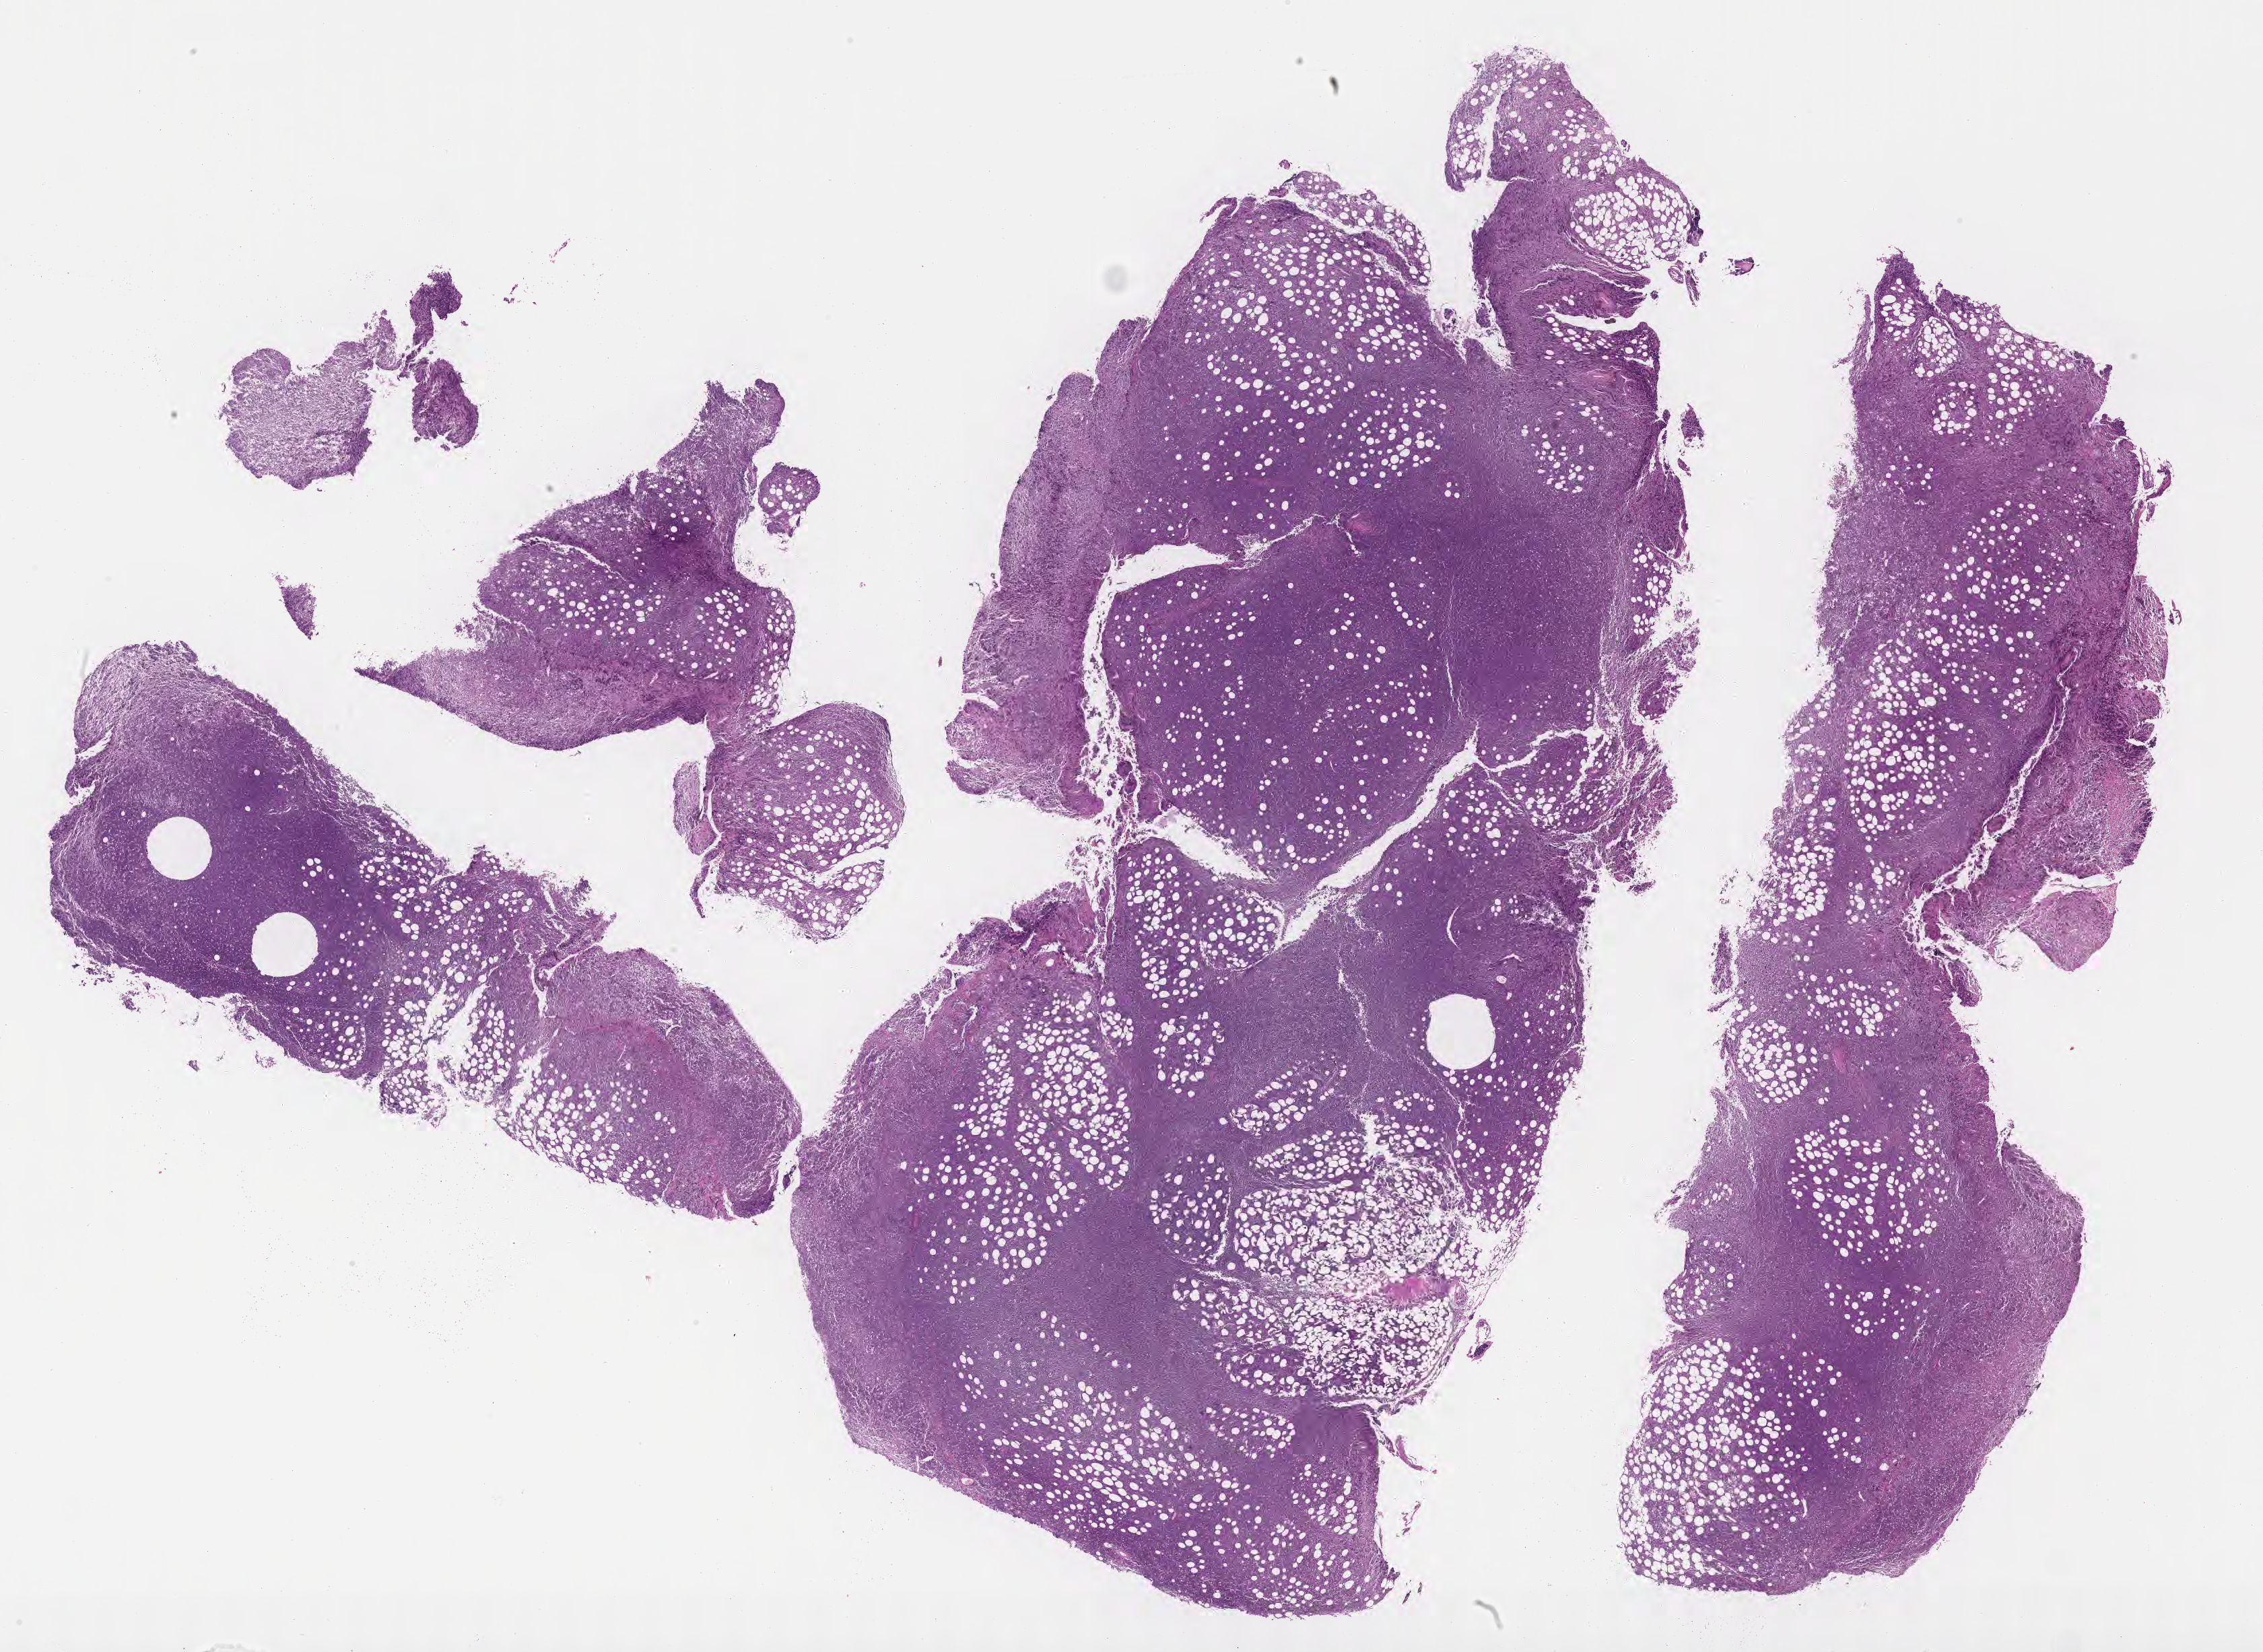
Digitized haematoxylin and eosin-stained section — low-resolution overview of the scanned area, about 27.2 x 19.8 mm, FFPE section, specimen: primary tumor. Male patient, 31 years old. Composition of this section per pathologist review: tumor cells 85%, tumor nuclei 95%, stromal cells 5%, necrosis 5%, normal cells 5%. Infiltration values recorded for this section: lymphocyte infiltration 40%, monocyte infiltration 30%, neutrophil infiltration 5%.
Histologic diagnosis: Burkitt lymphoma, NOS. Ann Arbor stage (patient): Stage IV. Section: top of the tissue portion.